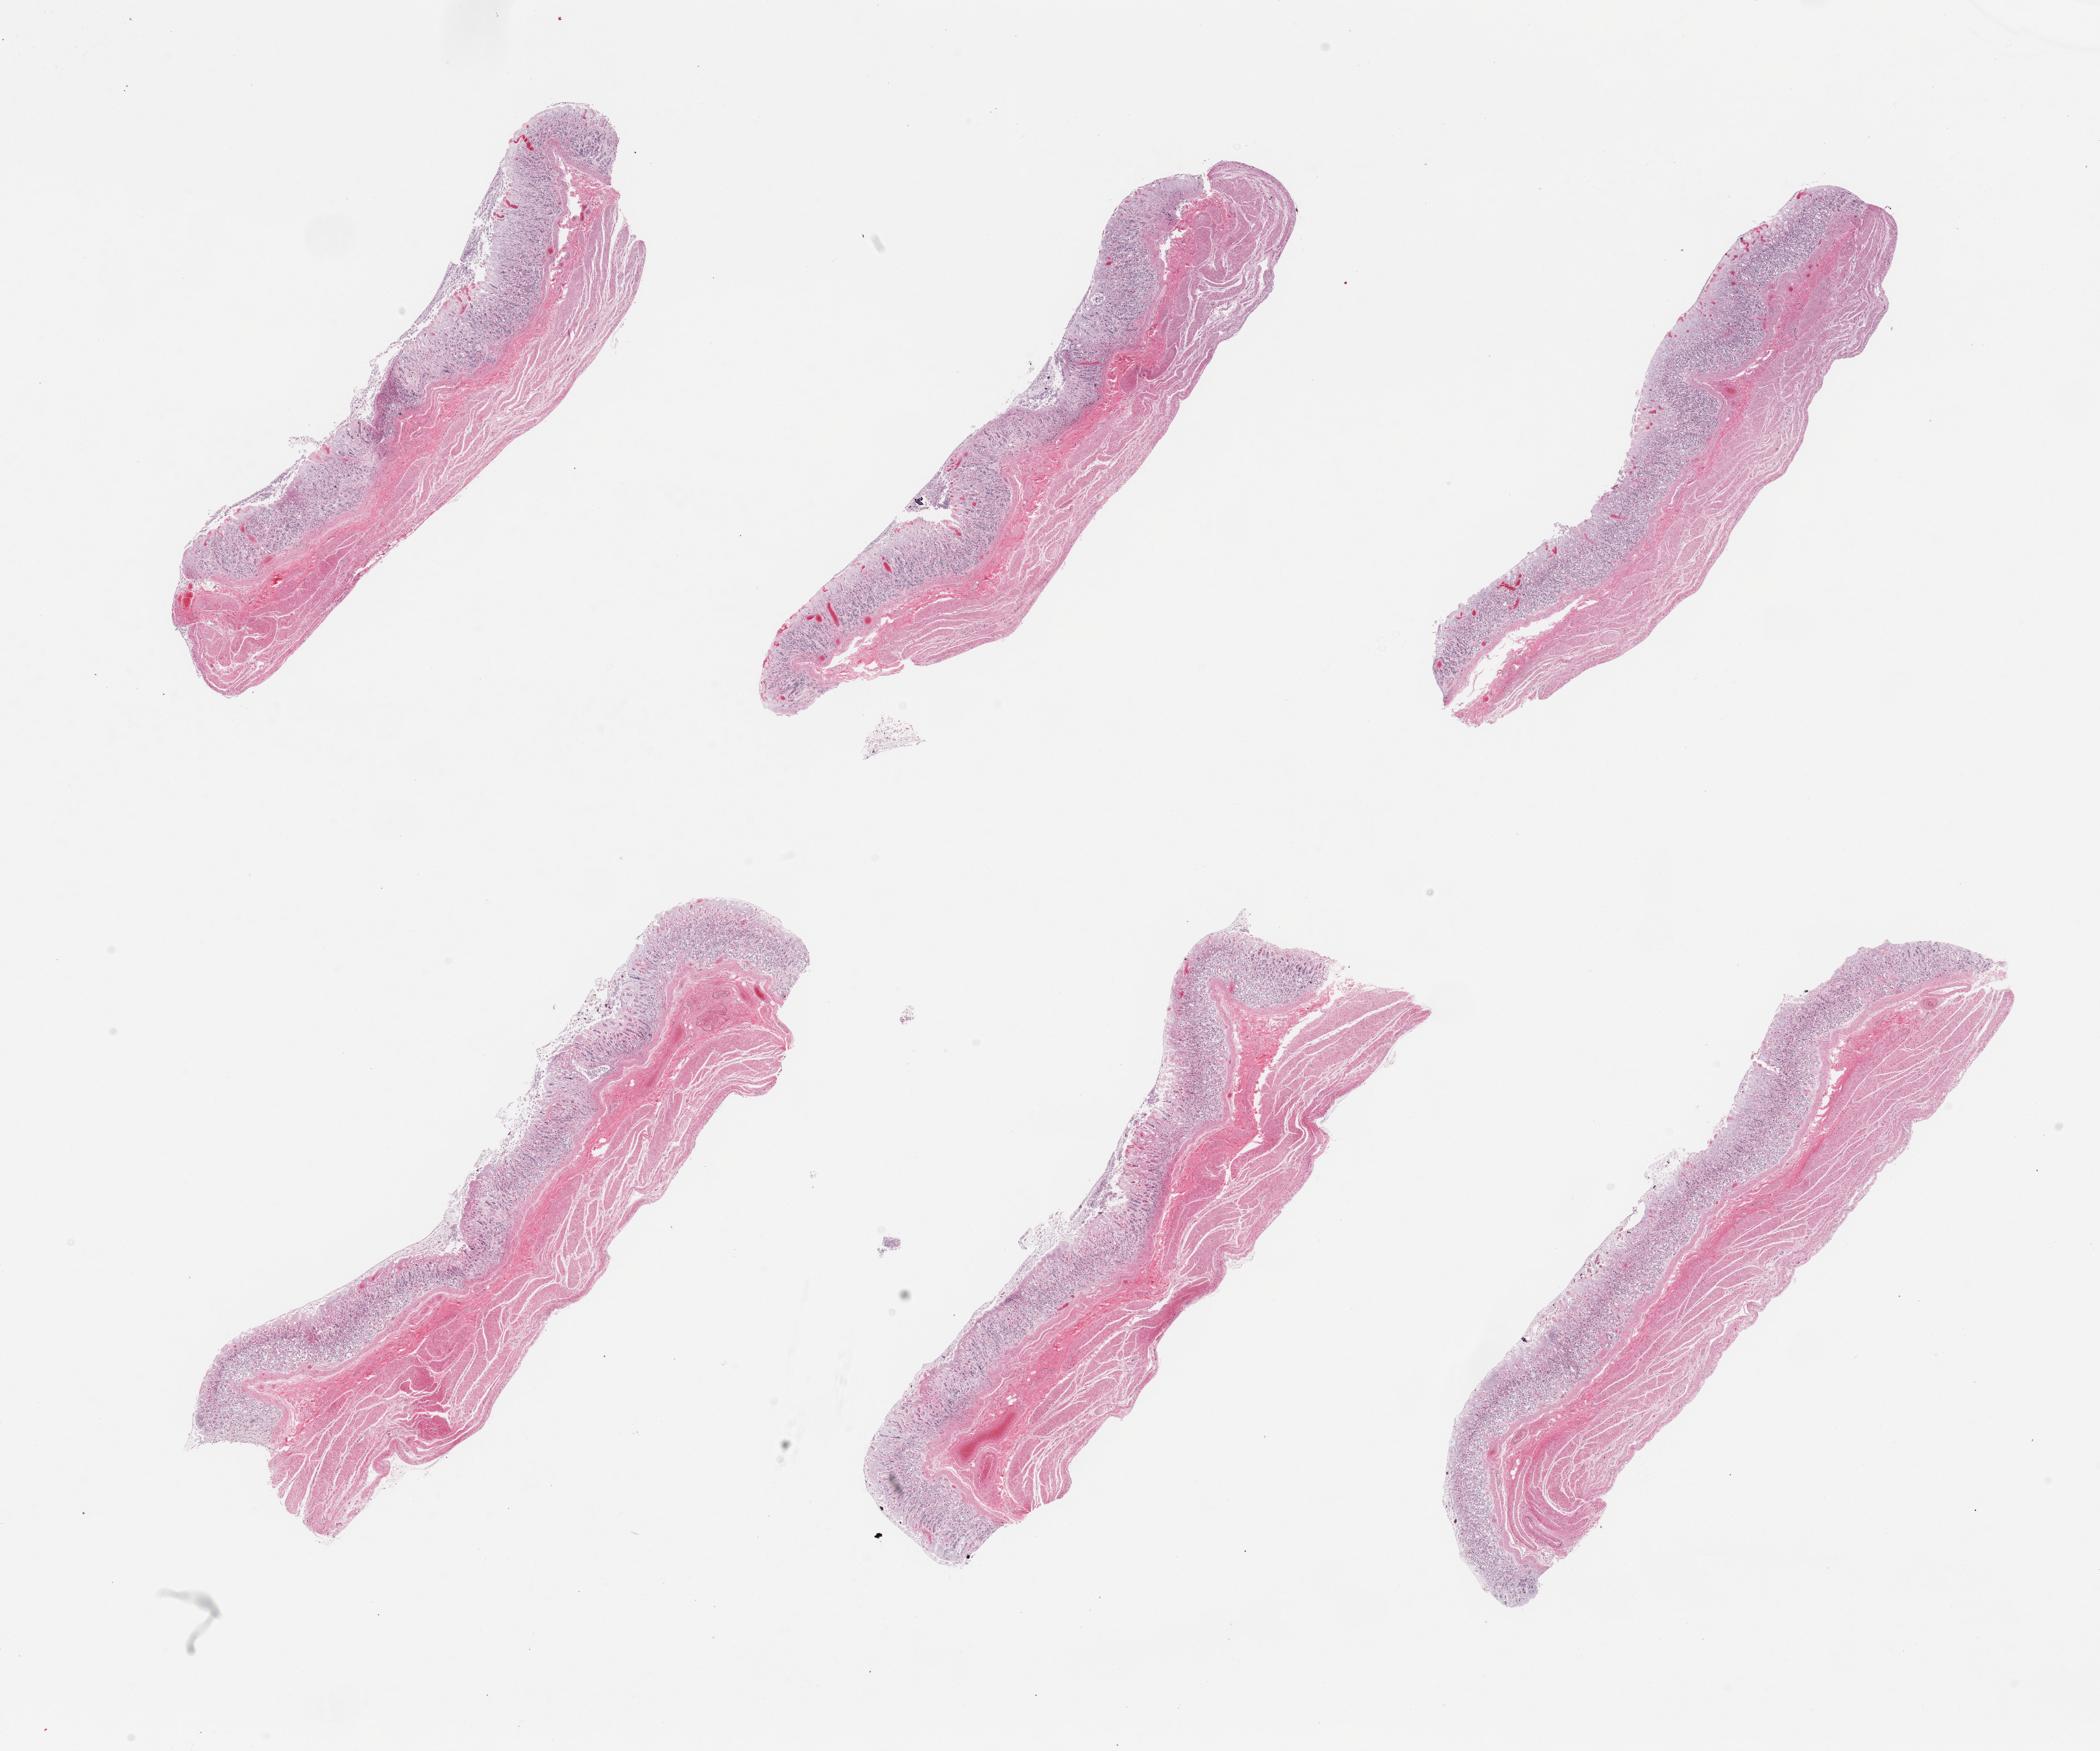
Whole-slide image, hematoxylin and eosin (H&E) stain, whole scanned area (about 25.6 x 21.3 mm, slide scanned at 20x) shown as a low-resolution overview, PAXgene-fixed, paraffin-embedded tissue, sampled site (target tissue): stomach, donor tissue sample. Donor sex: male.
* reviewer comment on this tissue sample: 6 pieces; mucosa severely autolyzed; muscularis moderately autolyzed; specimen of limited value; exogenous crystals (probably medication) in mucosa